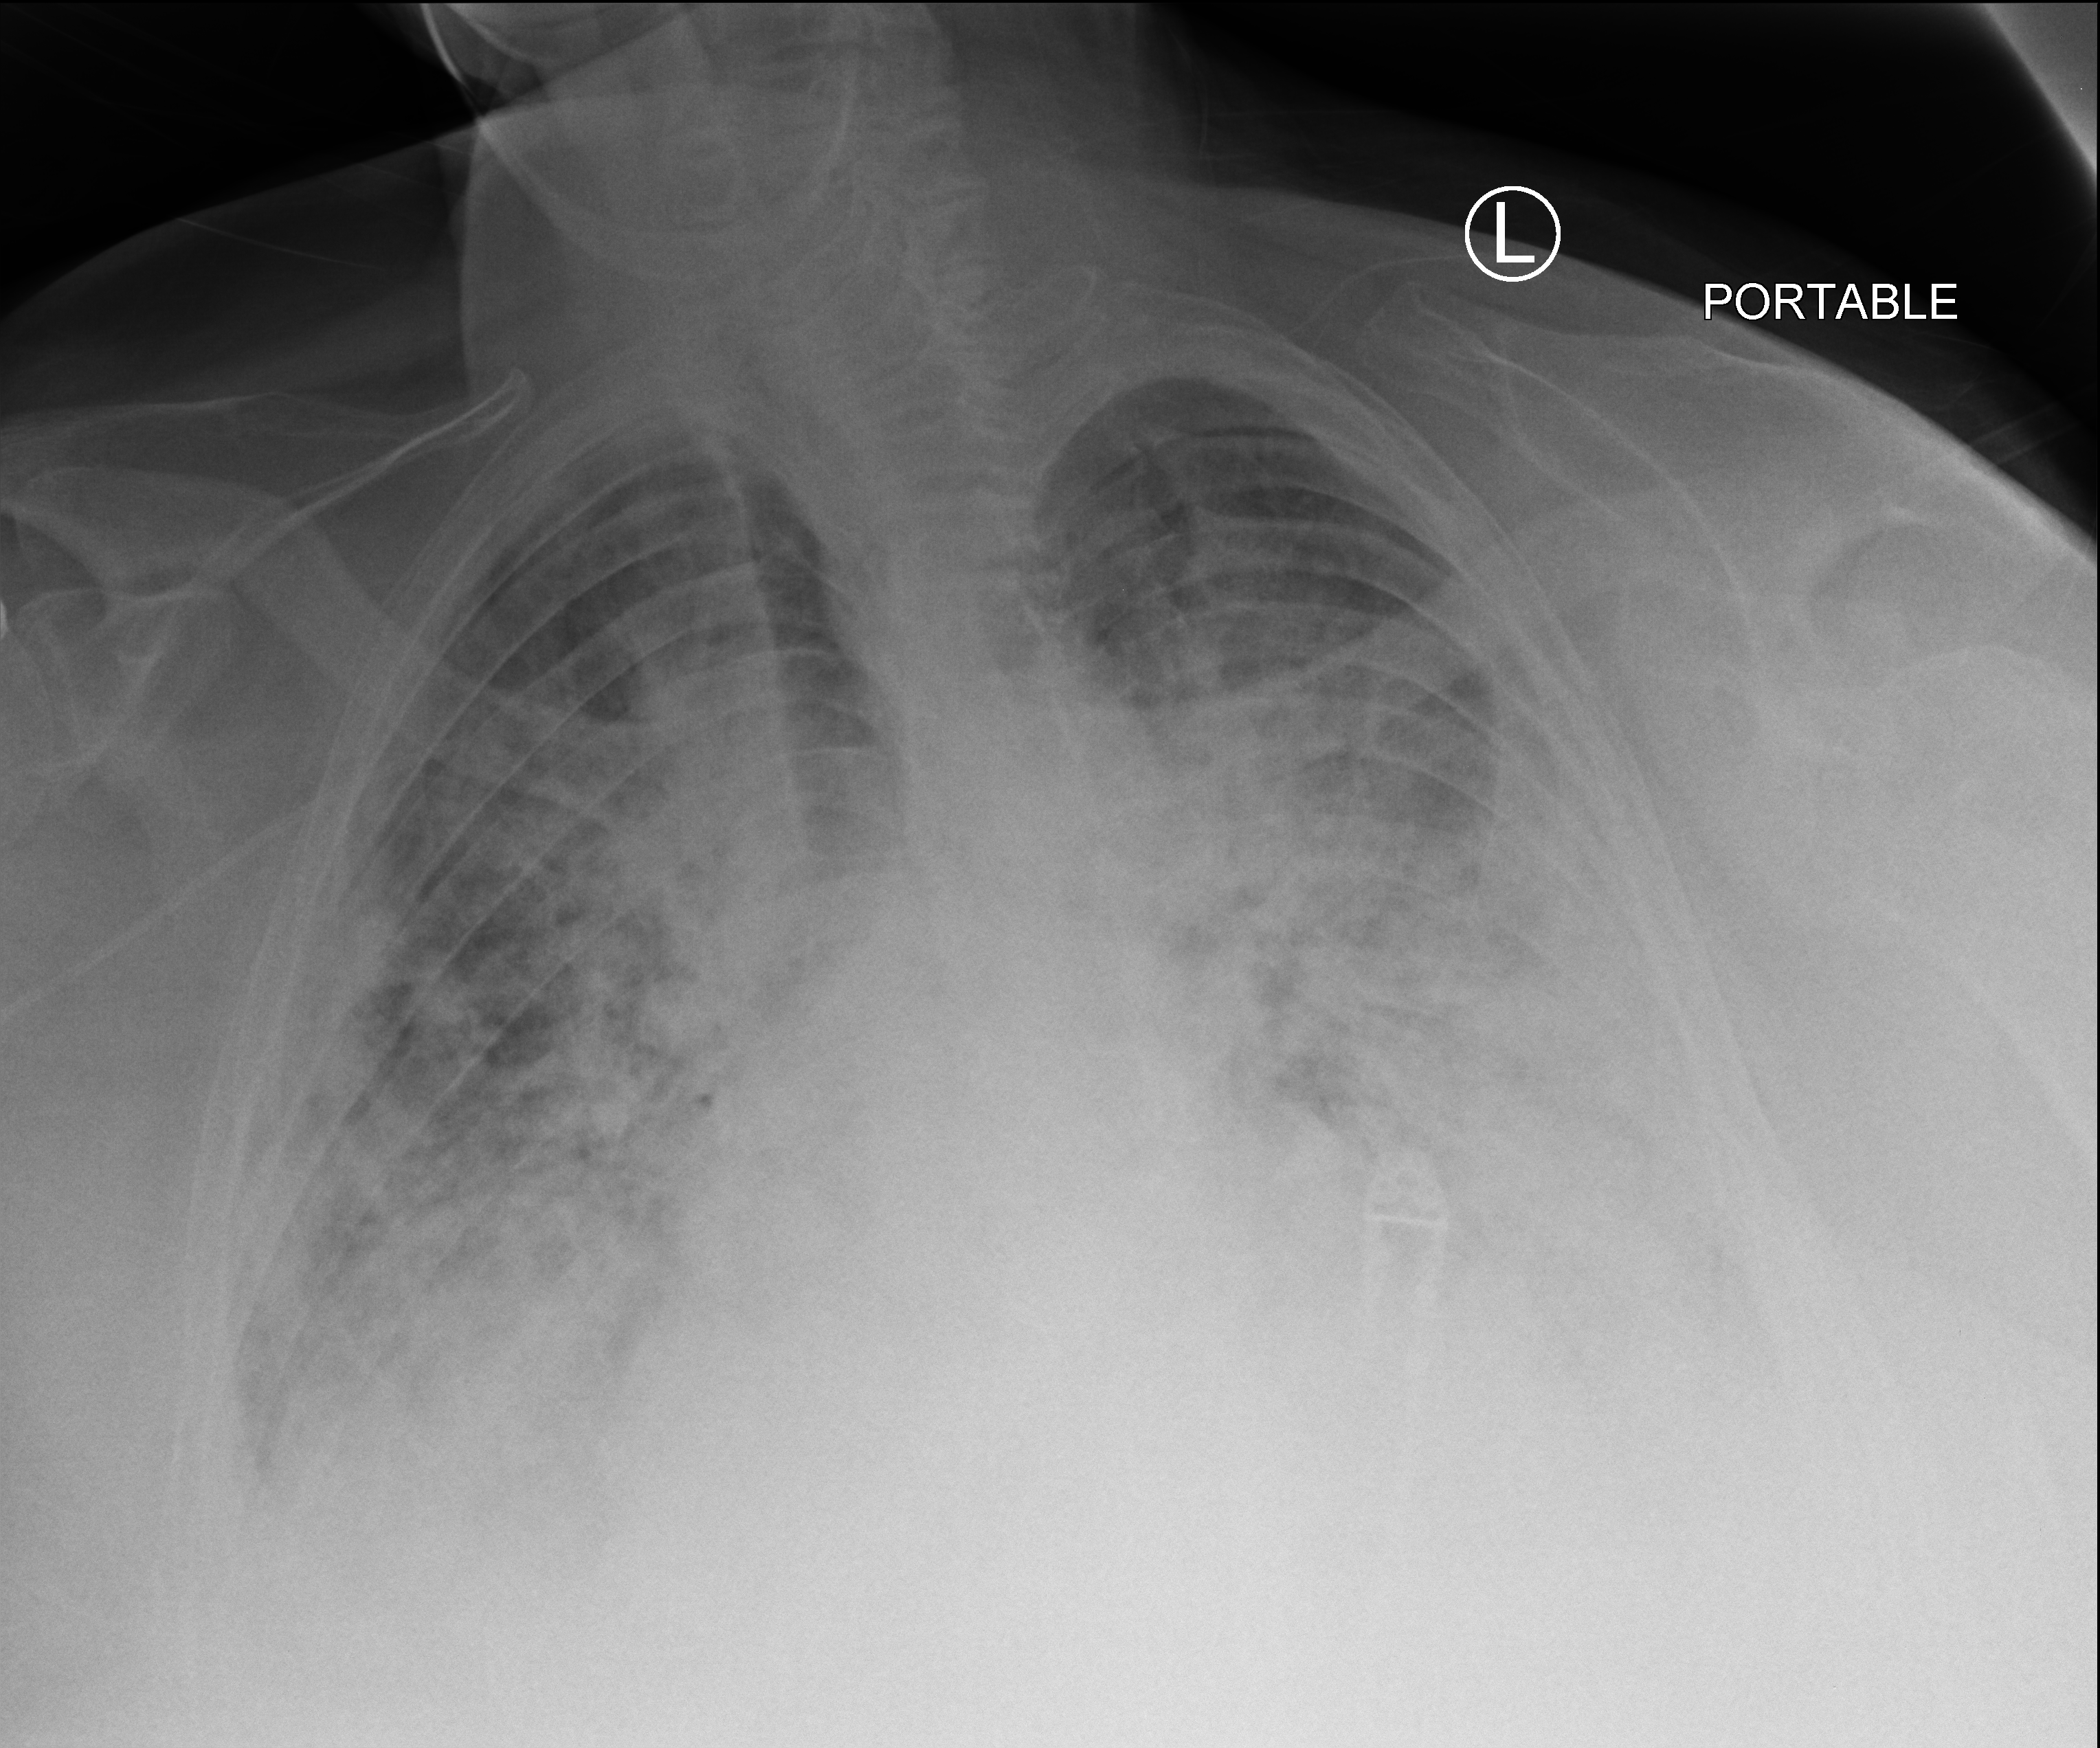
Bedside chest radiograph (computed radiography); anteroposterior (AP) projection. Patient hospitalised with COVID-19; male, aged 60–74 years.
Hospital-stay facts (about this admission, not read from this image; timing relative to this image not recorded):
- mechanically ventilated during this hospital stay: yes